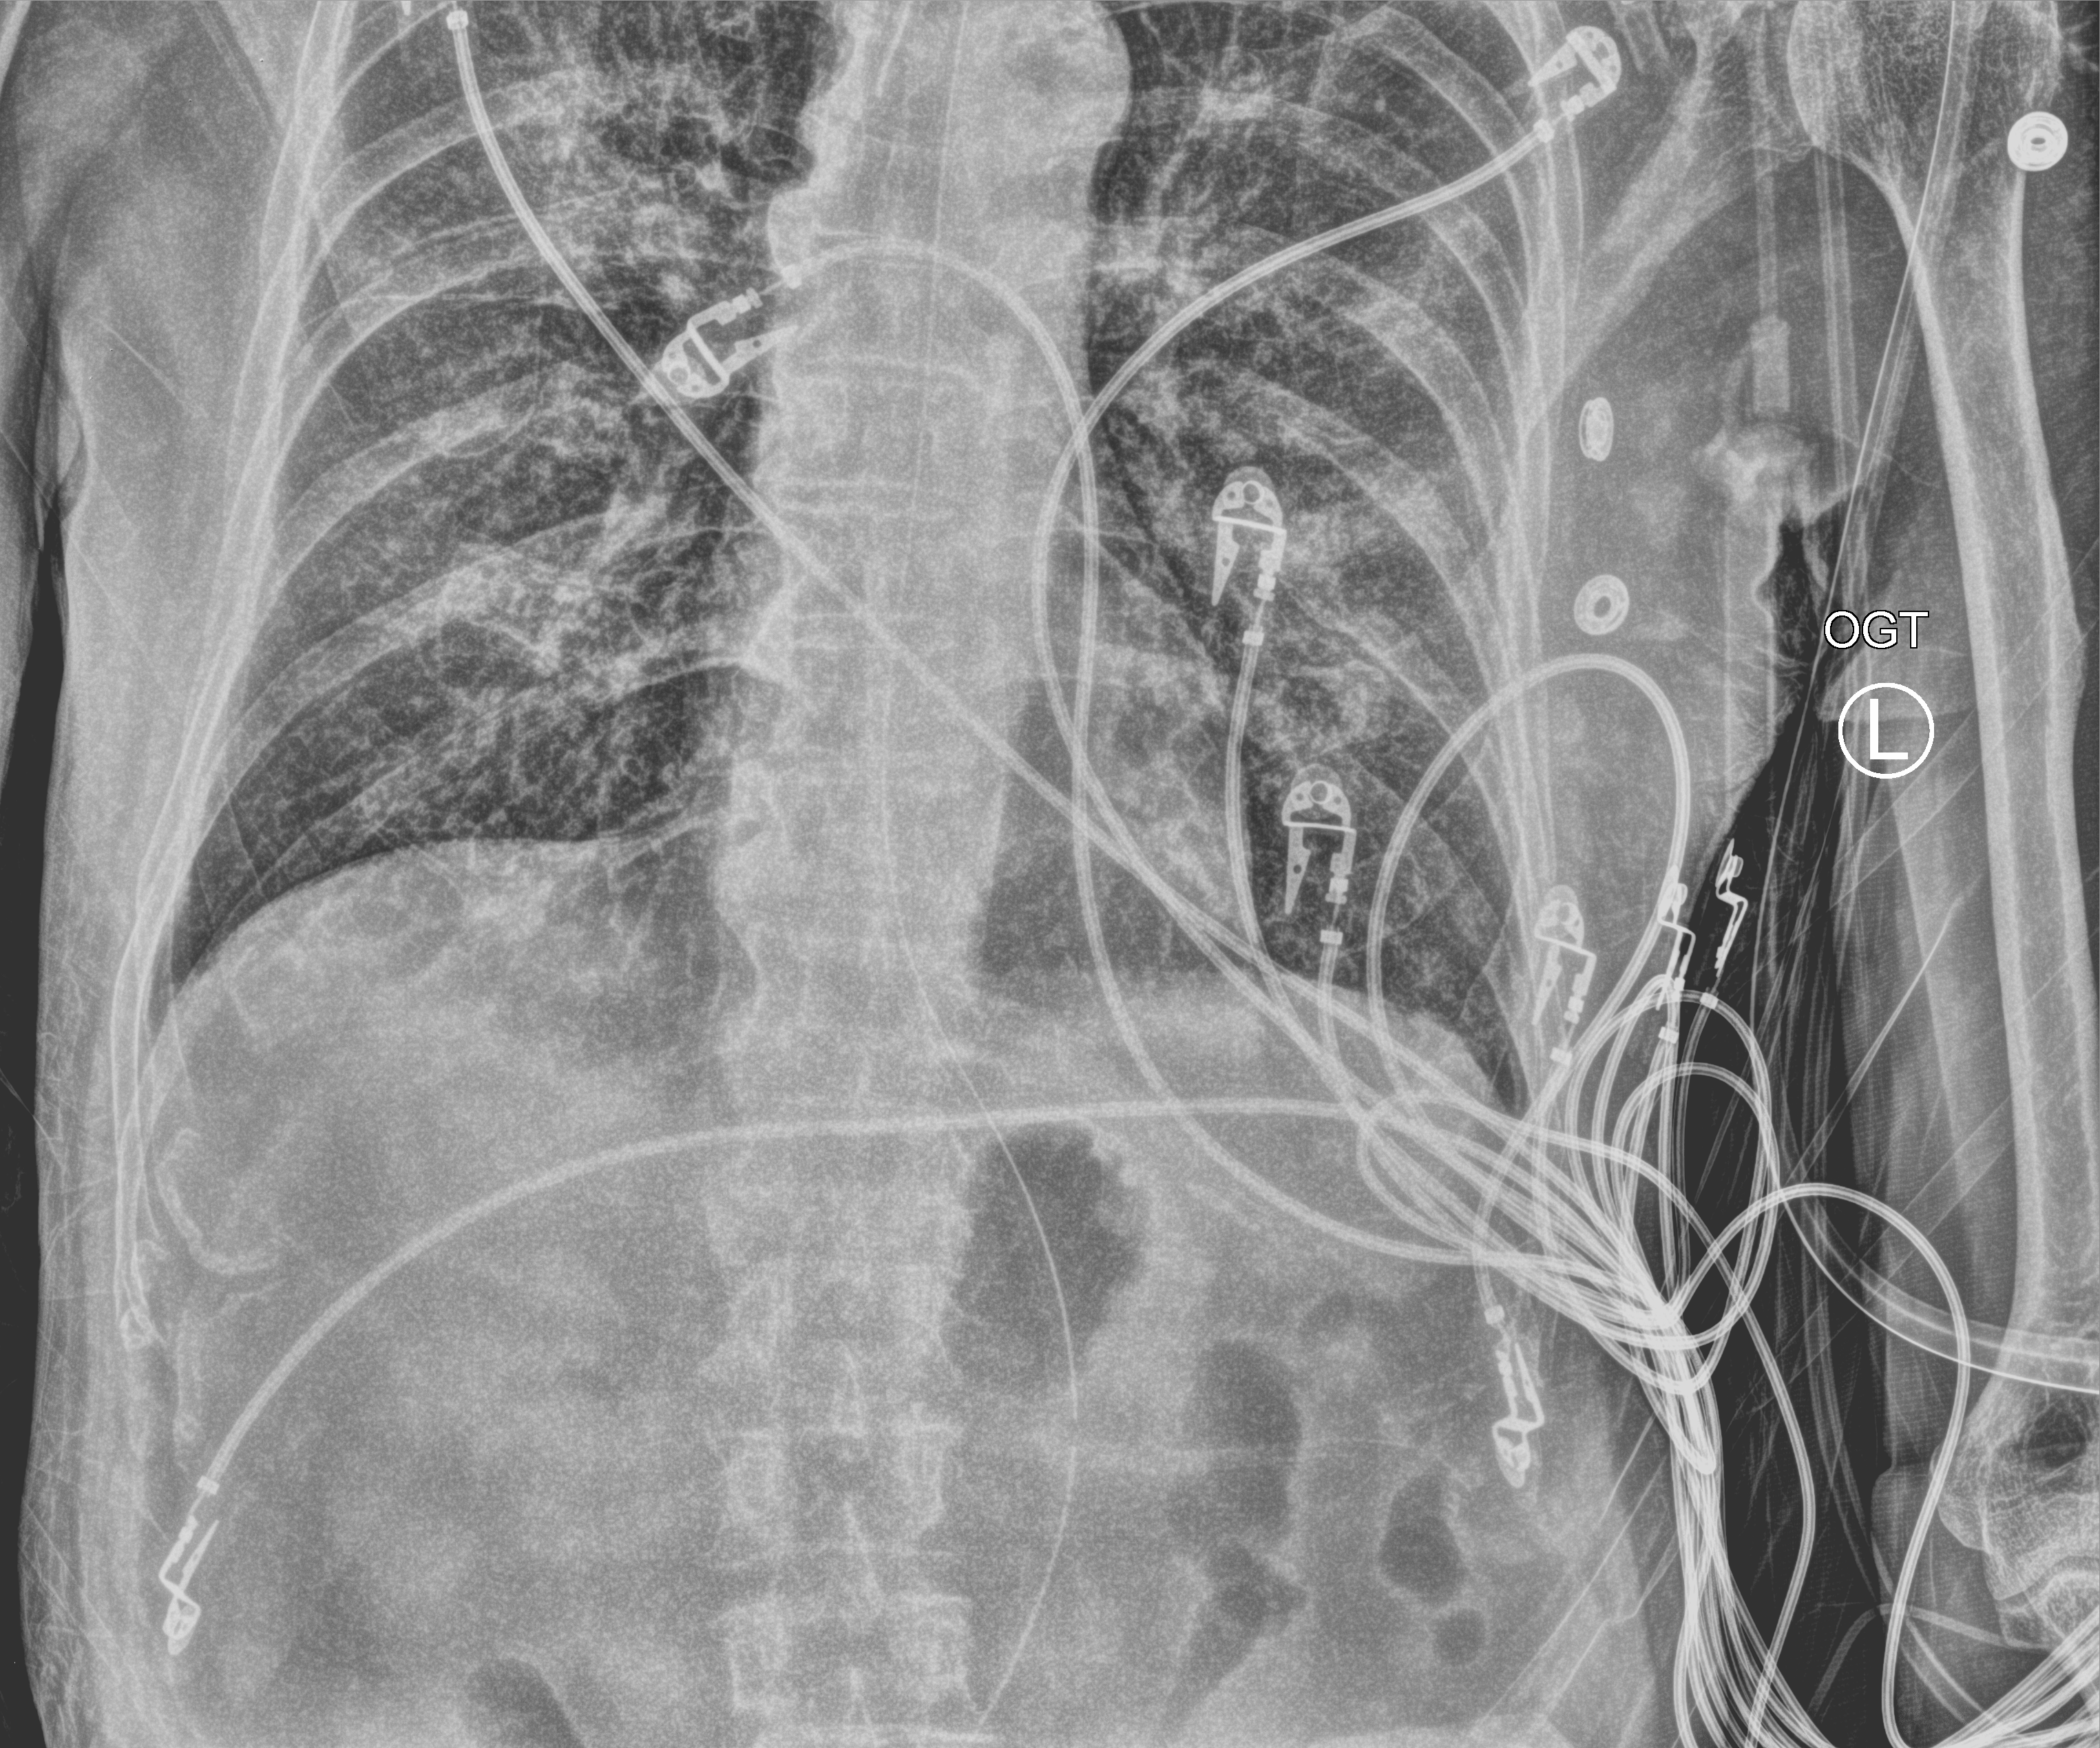
Bedside chest radiograph (computed radiography); anteroposterior (AP) projection. Patient hospitalised with COVID-19; male, aged 60–74 years.
From the hospital-stay record, not from the radiograph (when in the stay this image was taken is not recorded): diabetes (admission record): yes; admitted to intensive care during this hospital stay: yes; length of hospital stay: 42 days.